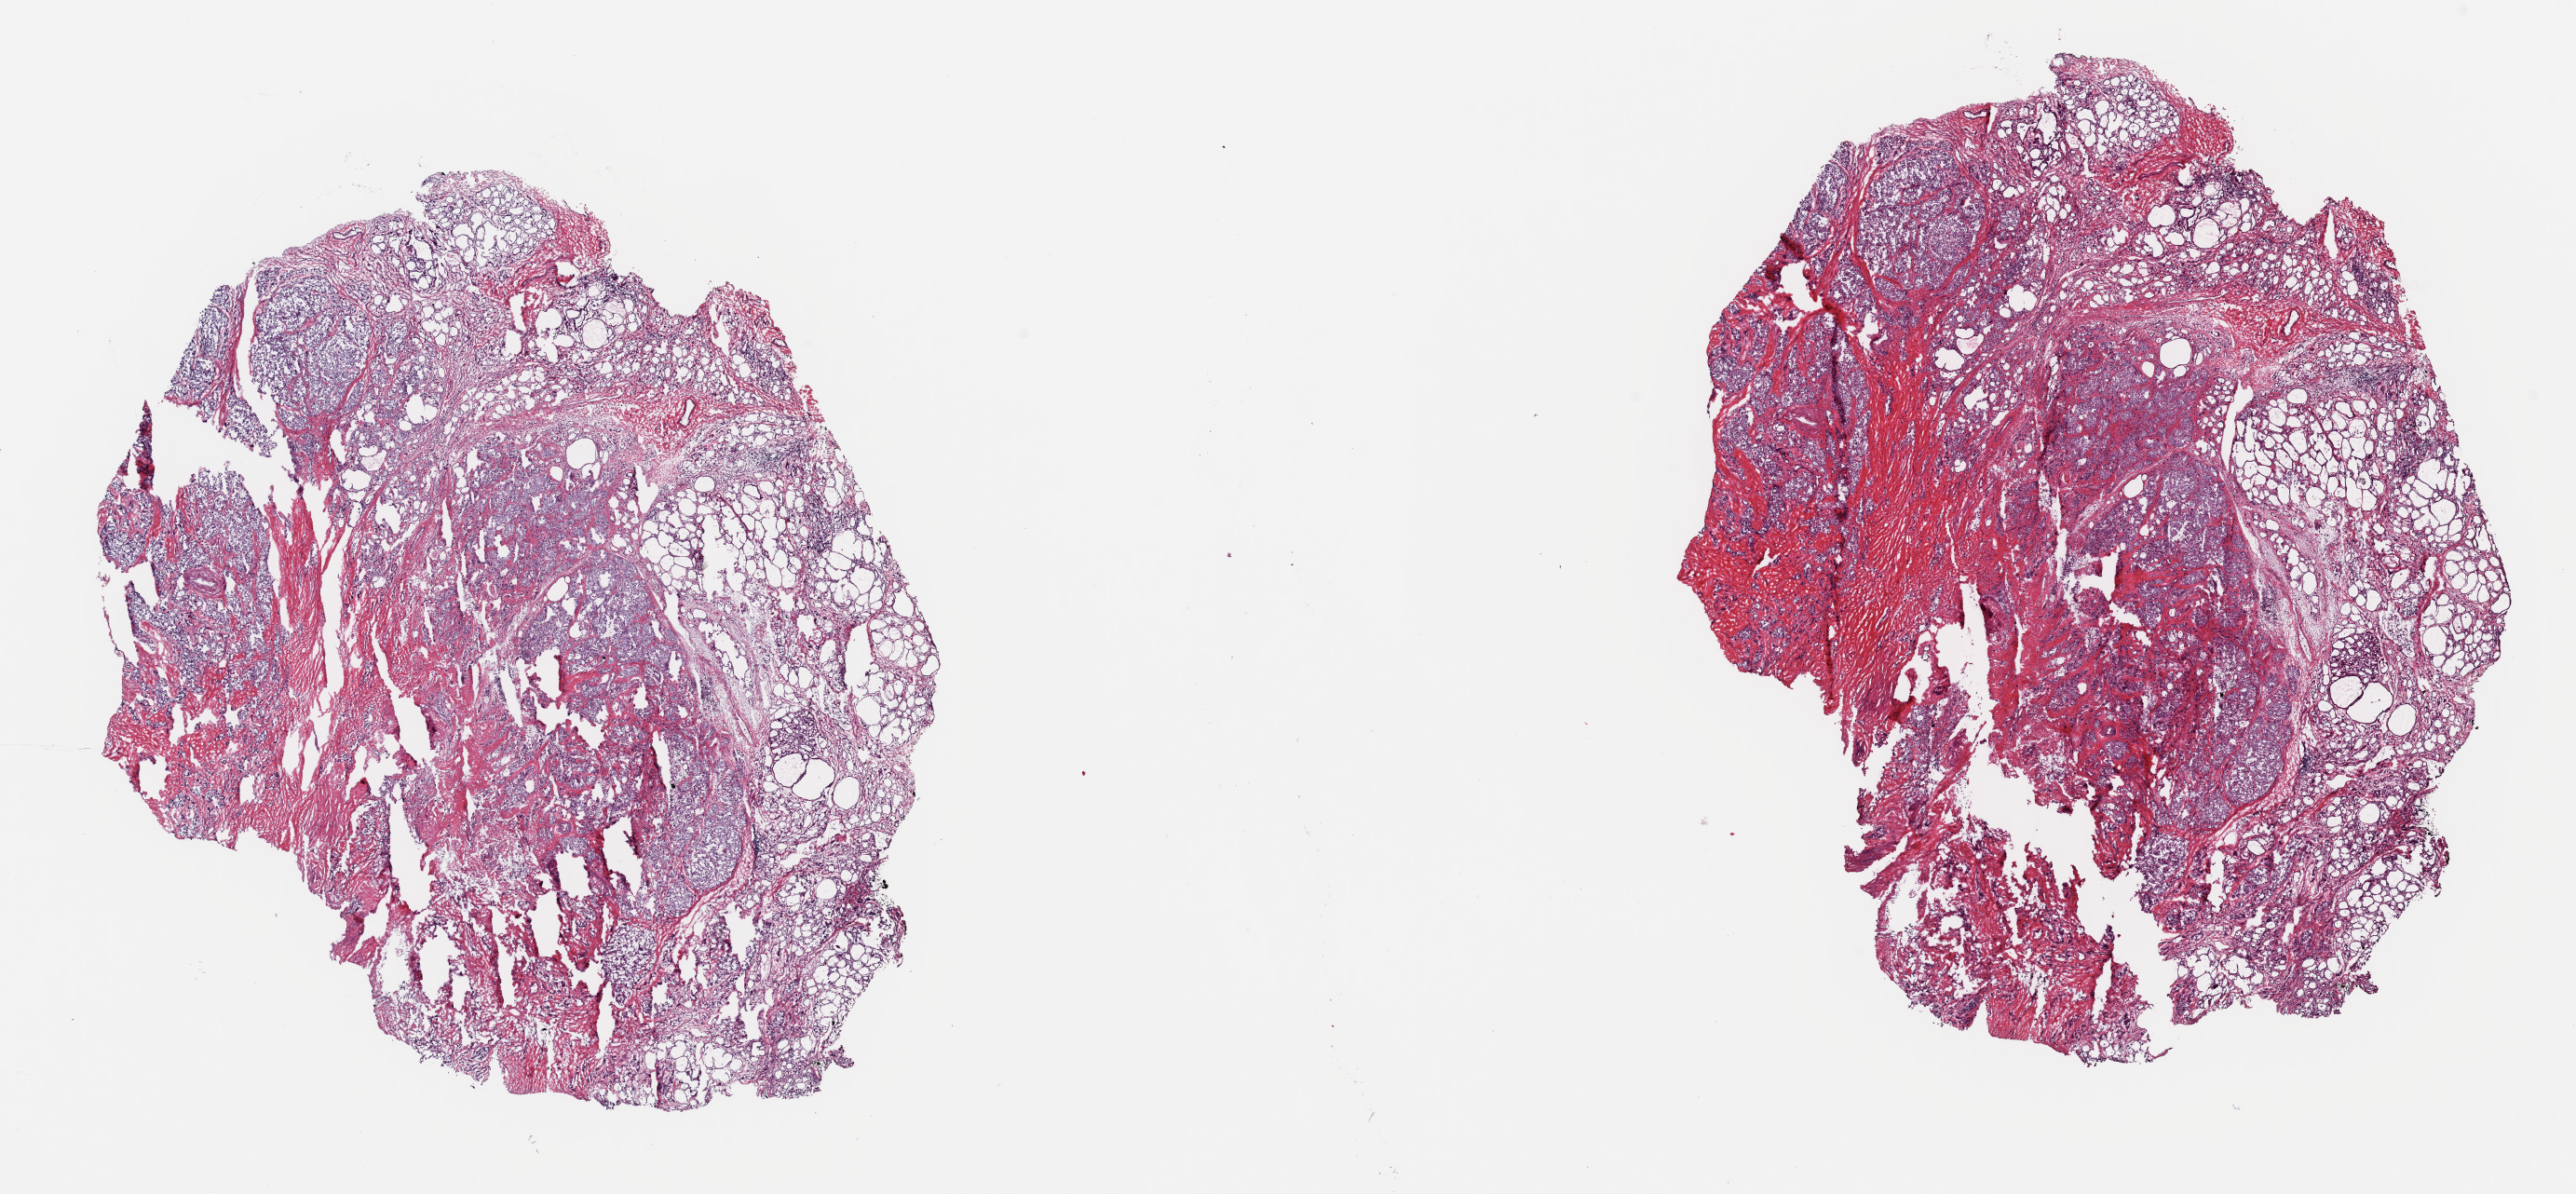
Hematoxylin and eosin (H&E) stained whole-slide image, low-resolution overview of the scanned area, about 21.9 x 10.1 mm (from a 40x scan). Frozen section from the top of the tissue portion. Primary tumour sample from the thyroid. Female patient; age at initial diagnosis 43 years. Composition of this section per pathologist review: tumour cells 65%, tumour nuclei 65%, normal cells 25%, stromal cells 10%, necrosis 0%. Inflammatory infiltration, as recorded: lymphocyte infiltration 0%, monocyte infiltration 0%, neutrophil infiltration 0%.
AJCC pathologic stage: I. TNM: T1 N0 MX. Diagnosis: Papillary carcinoma, follicular variant (thyroid gland). Lymph nodes positive (case pathology): 0 of 2 examined.